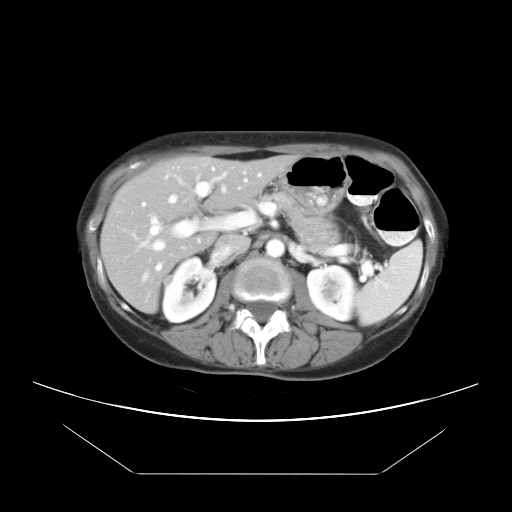
Contrast-enhanced abdominal CT, one axial slice. Slice 11 of 21 in the series (ordered by position). Reconstruction kernel STANDARD. 120 kVp. Intravenous contrast given. Soft-tissue window (W 400 / L 40 HU). 7.5 mm slice thickness. 512 × 512 image matrix. Female patient, age 72 years. Case-level facts recorded for this patient, not image findings: diagnosis: colorectal cancer liver metastases, imaged before liver resection; multiple liver metastases: yes.
Outlined on this slice (manually delineated by an expert):
- hepatic veins: box from (x=139, y=169) to (x=246, y=252) px
- liver: (x=102, y=156)–(x=292, y=312)
- planned liver remnant (the part of the liver to remain after resection): (x=102, y=156)–(x=293, y=286)
- portal vein (with intrahepatic branches): (x=141, y=174)–(x=225, y=270)